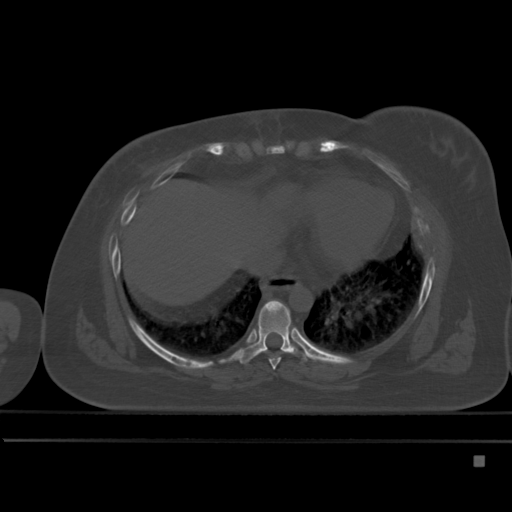
CT including the spine, one axial slice. Slice 282 of 495 in the series (ordered by position). Bone window (W 1800 / L 400 HU). 1.5 mm slice thickness. 512 × 512 image matrix. Patient: female, 33 years. Case-level facts recorded for this patient, not image findings: primary cancer: breast.
Annotated regions visible in this slice (semi-automatic segmentation, software-assisted and operator-edited):
- T7 vertebra: box from (x=269, y=327) to (x=296, y=370) px
- T8 vertebra: (x=233, y=300)–(x=309, y=364)